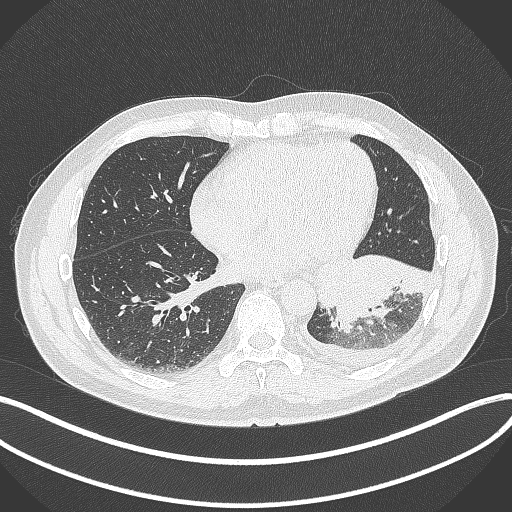
Chest CT, one axial slice. Position 130 of 342 along the scan axis. Reconstruction kernel B70f. Lung window (W 1500 / L -600 HU). 1 mm slice thickness. 512 × 512 image matrix. Patient: male, 58 years. Case-level facts recorded for this patient, not image findings: clinical TNM (as recorded): T3 N1 M1b; histopathological grade: G3.
Outlined on this slice (bounding box drawn by a radiologist):
- lung tumour (recorded histology: small cell carcinoma): box from (x=317, y=252) to (x=426, y=327) px